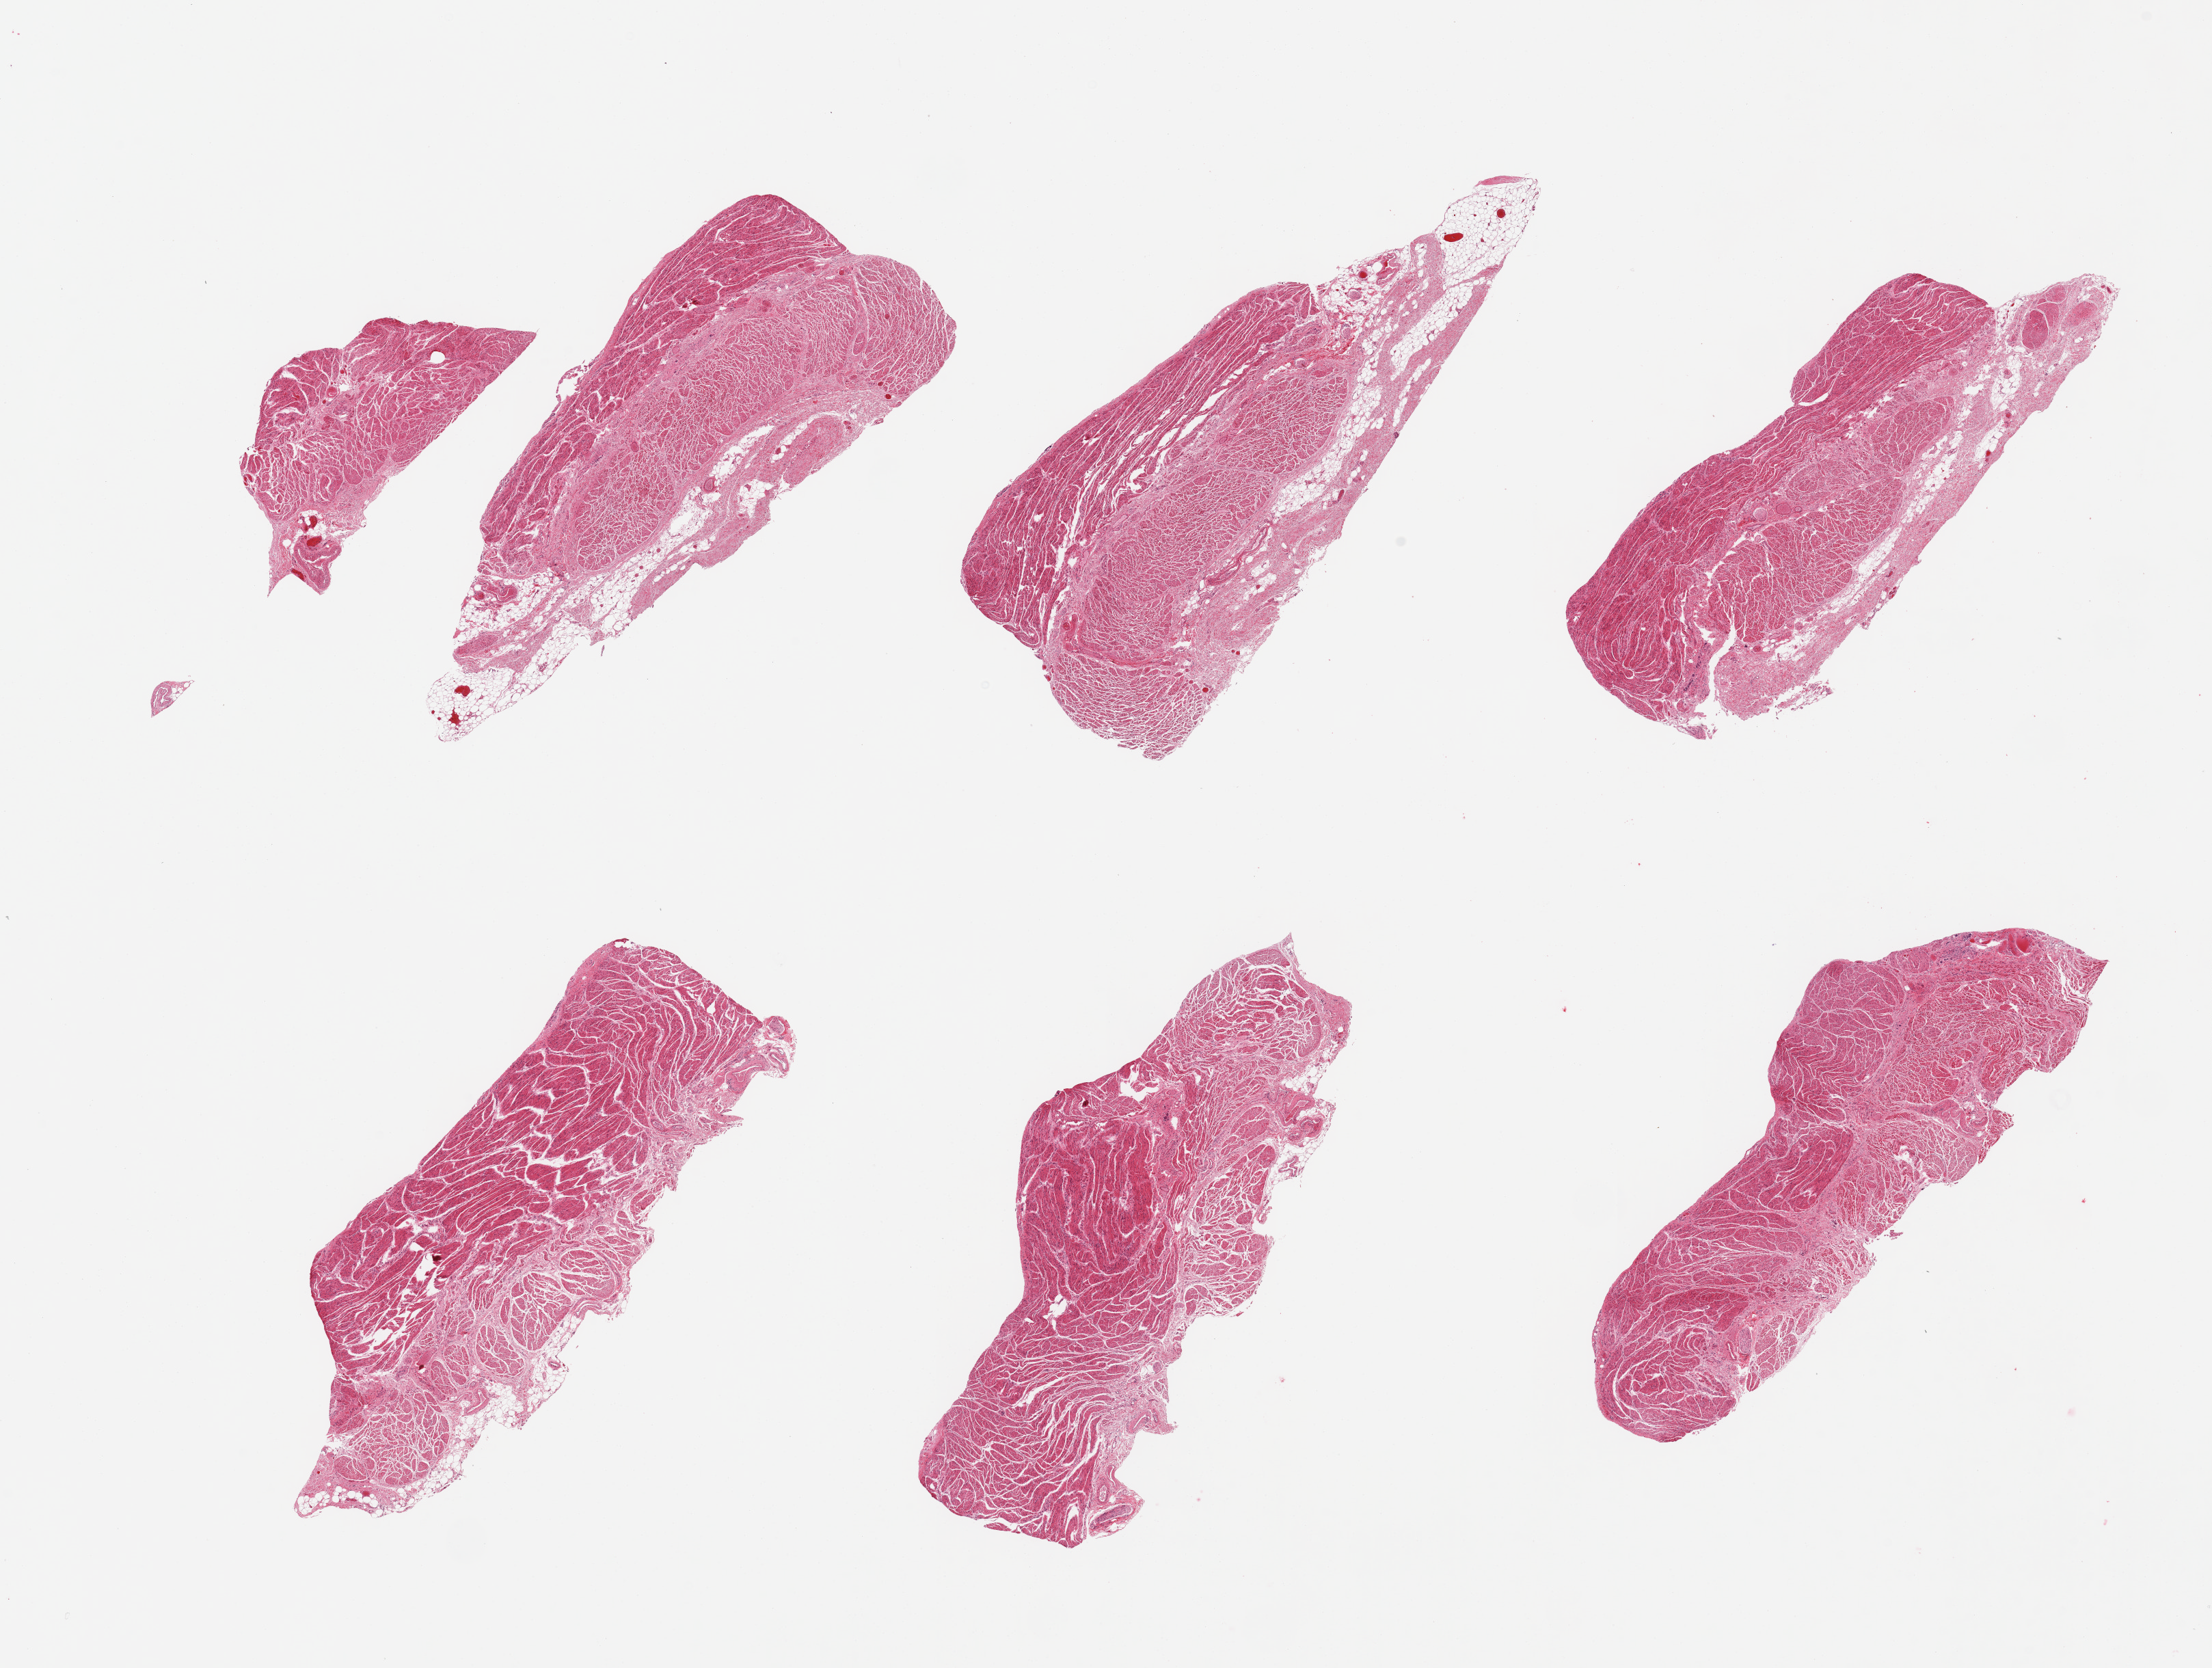
Digitized H&E-stained section, a low-resolution overview of the entire scanned area, about 25.6 x 19.3 mm (acquisition: 20x scan), PAXgene-fixed paraffin-embedded (PFPE) section, target tissue: gastroesophageal junction, donor tissue sample. Male donor.
• review note (as recorded): 6 pieces, all muscularis